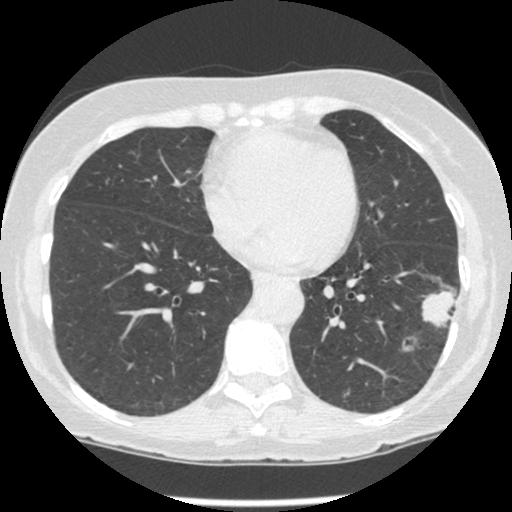
Low-dose screening chest CT, one axial slice. Slice 96 of 247 in the series (ordered by position). 120 kVp. Lung window (W 1500 / L -600 HU). 1.25 mm slice thickness. 512 × 512 image matrix, field of view 303 × 303 mm.
Structures marked on this image (expert manual segmentation):
- lesion 1 (tumor, lower lobe of left lung): bounding box [x1, y1, x2, y2] px = [422, 290, 455, 327]